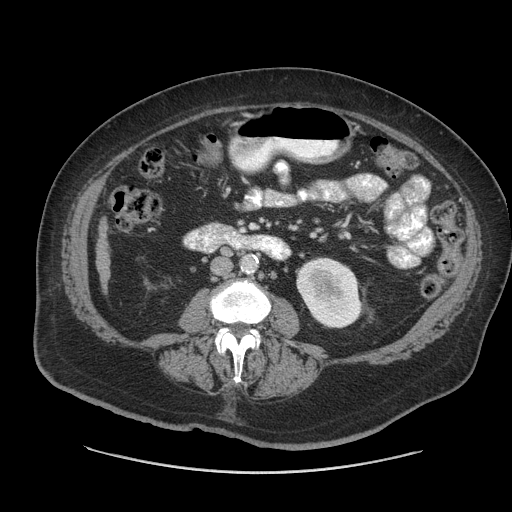
Contrast-enhanced abdominal CT (liver protocol), one axial slice. Position 9 of 91 along the scan axis. Soft-tissue window (W 400 / L 40 HU). 2.5 mm slice thickness. 512 × 512 image matrix, field of view 420 × 420 mm. Case-level facts recorded for this patient, not image findings: diagnosis: hepatocellular carcinoma (patient treated with transarterial chemoembolisation; whether this scan precedes or follows treatment is not stated here); TNM stage (as recorded): Stage-I; Child-Pugh class: A; tumour differentiation: well differentiated; tumour nodularity: uninodular.
Outlined on this slice (semi-automatically segmented with operator editing):
- liver parenchyma outside the tumour (the mass and vessels are separate outlines, so this box may not span the whole liver): bounding box <96,222,110,291> (left, top, right, bottom; pixels)